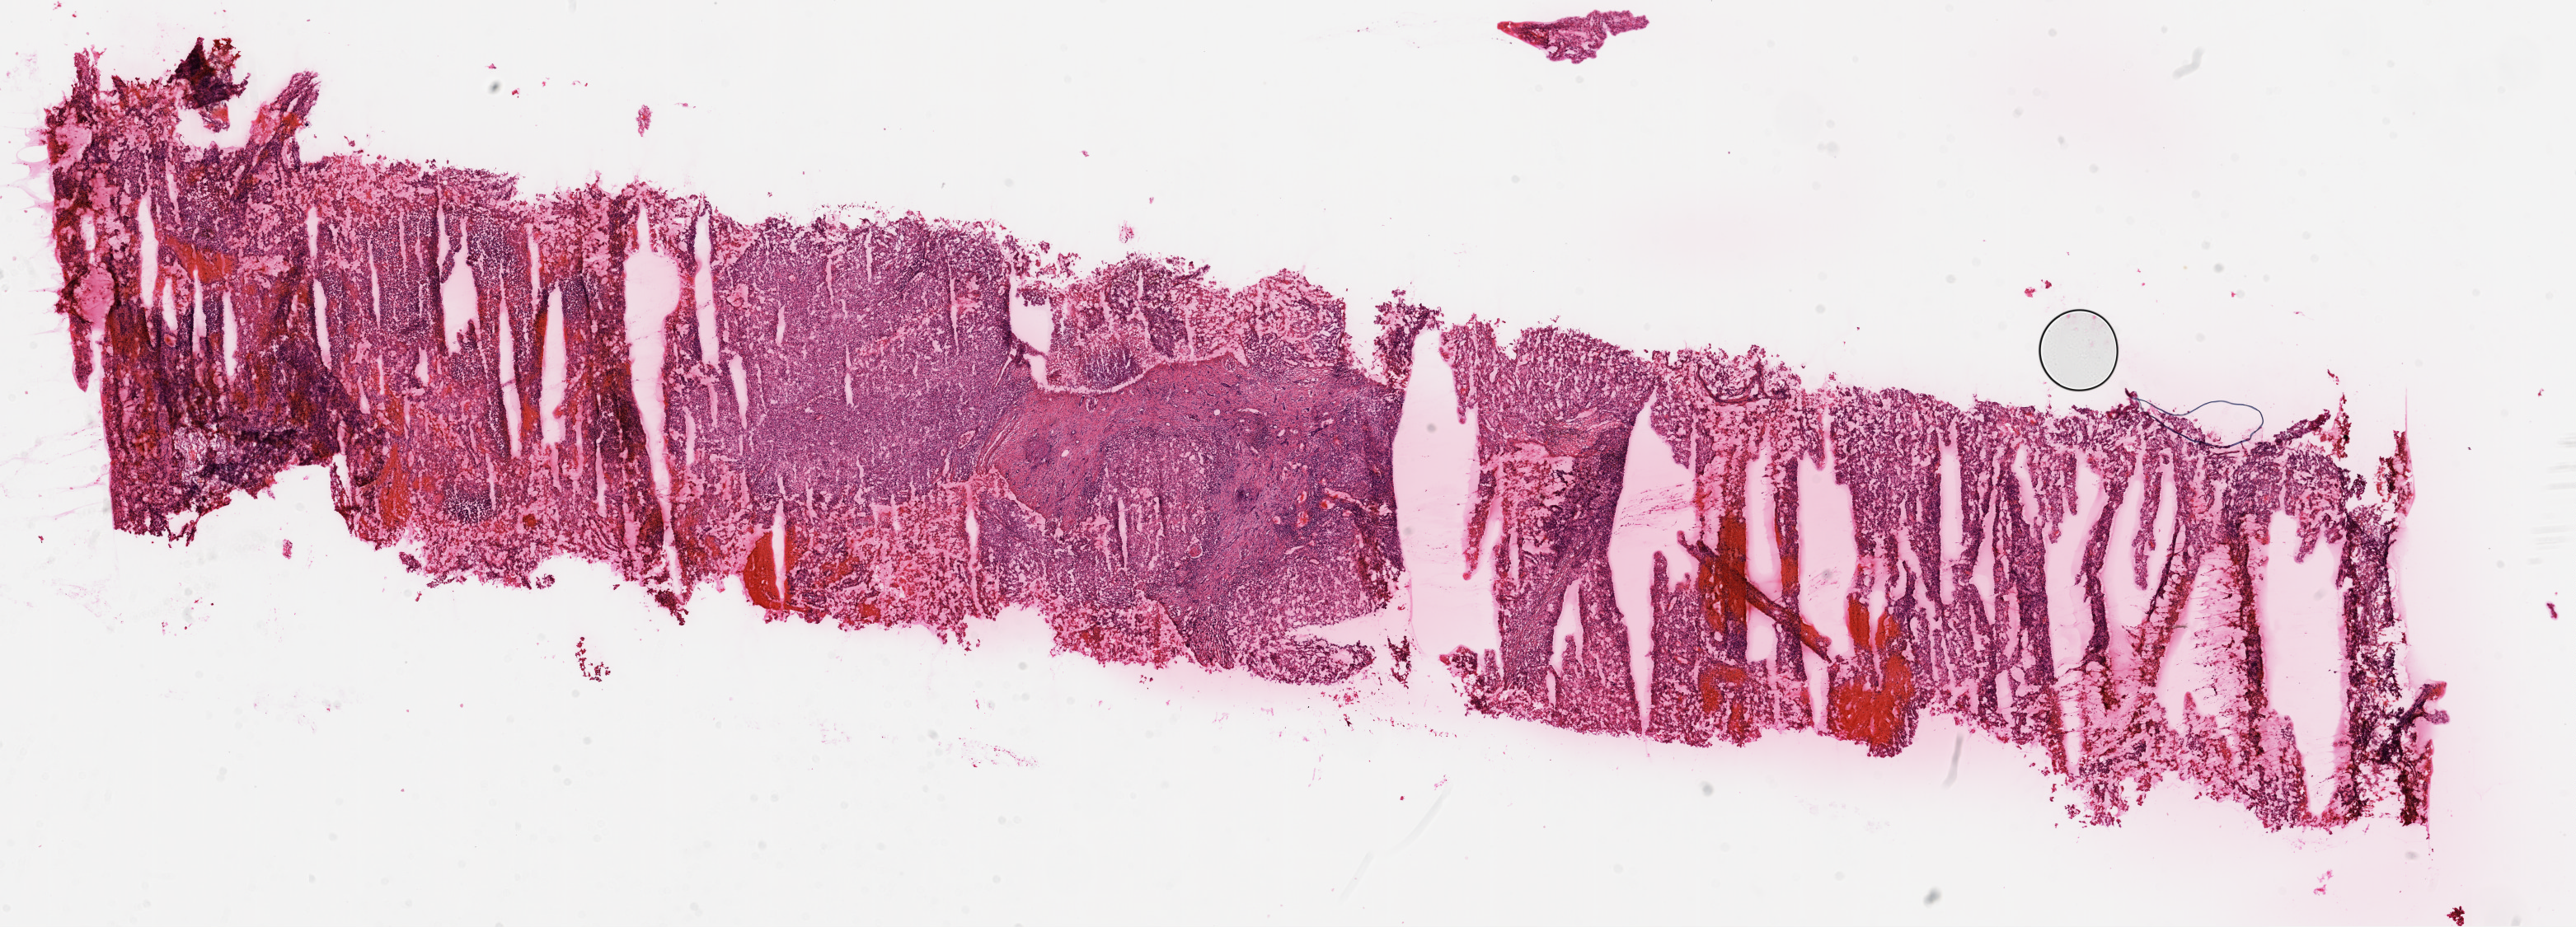
Digitized H&E tissue section (whole slide), shown as a low-resolution overview of the whole scanned area (about 25.1 x 9.0 mm, from a 20x scan), frozen section from the top of the tissue portion, primary tumour sample from the kidney. Female patient; age at initial diagnosis 57 years. Histologic grade: G4 (undifferentiated). Slide review estimates, as recorded: tumour cells 80%, tumour nuclei 75%, normal cells 0%, stromal cells 15%, necrosis 5%.
AJCC pathologic stage: III (7th edition). Lymph nodes positive (case pathology): 0 of 5 examined. Pathologic diagnosis: Clear cell adenocarcinoma, NOS.